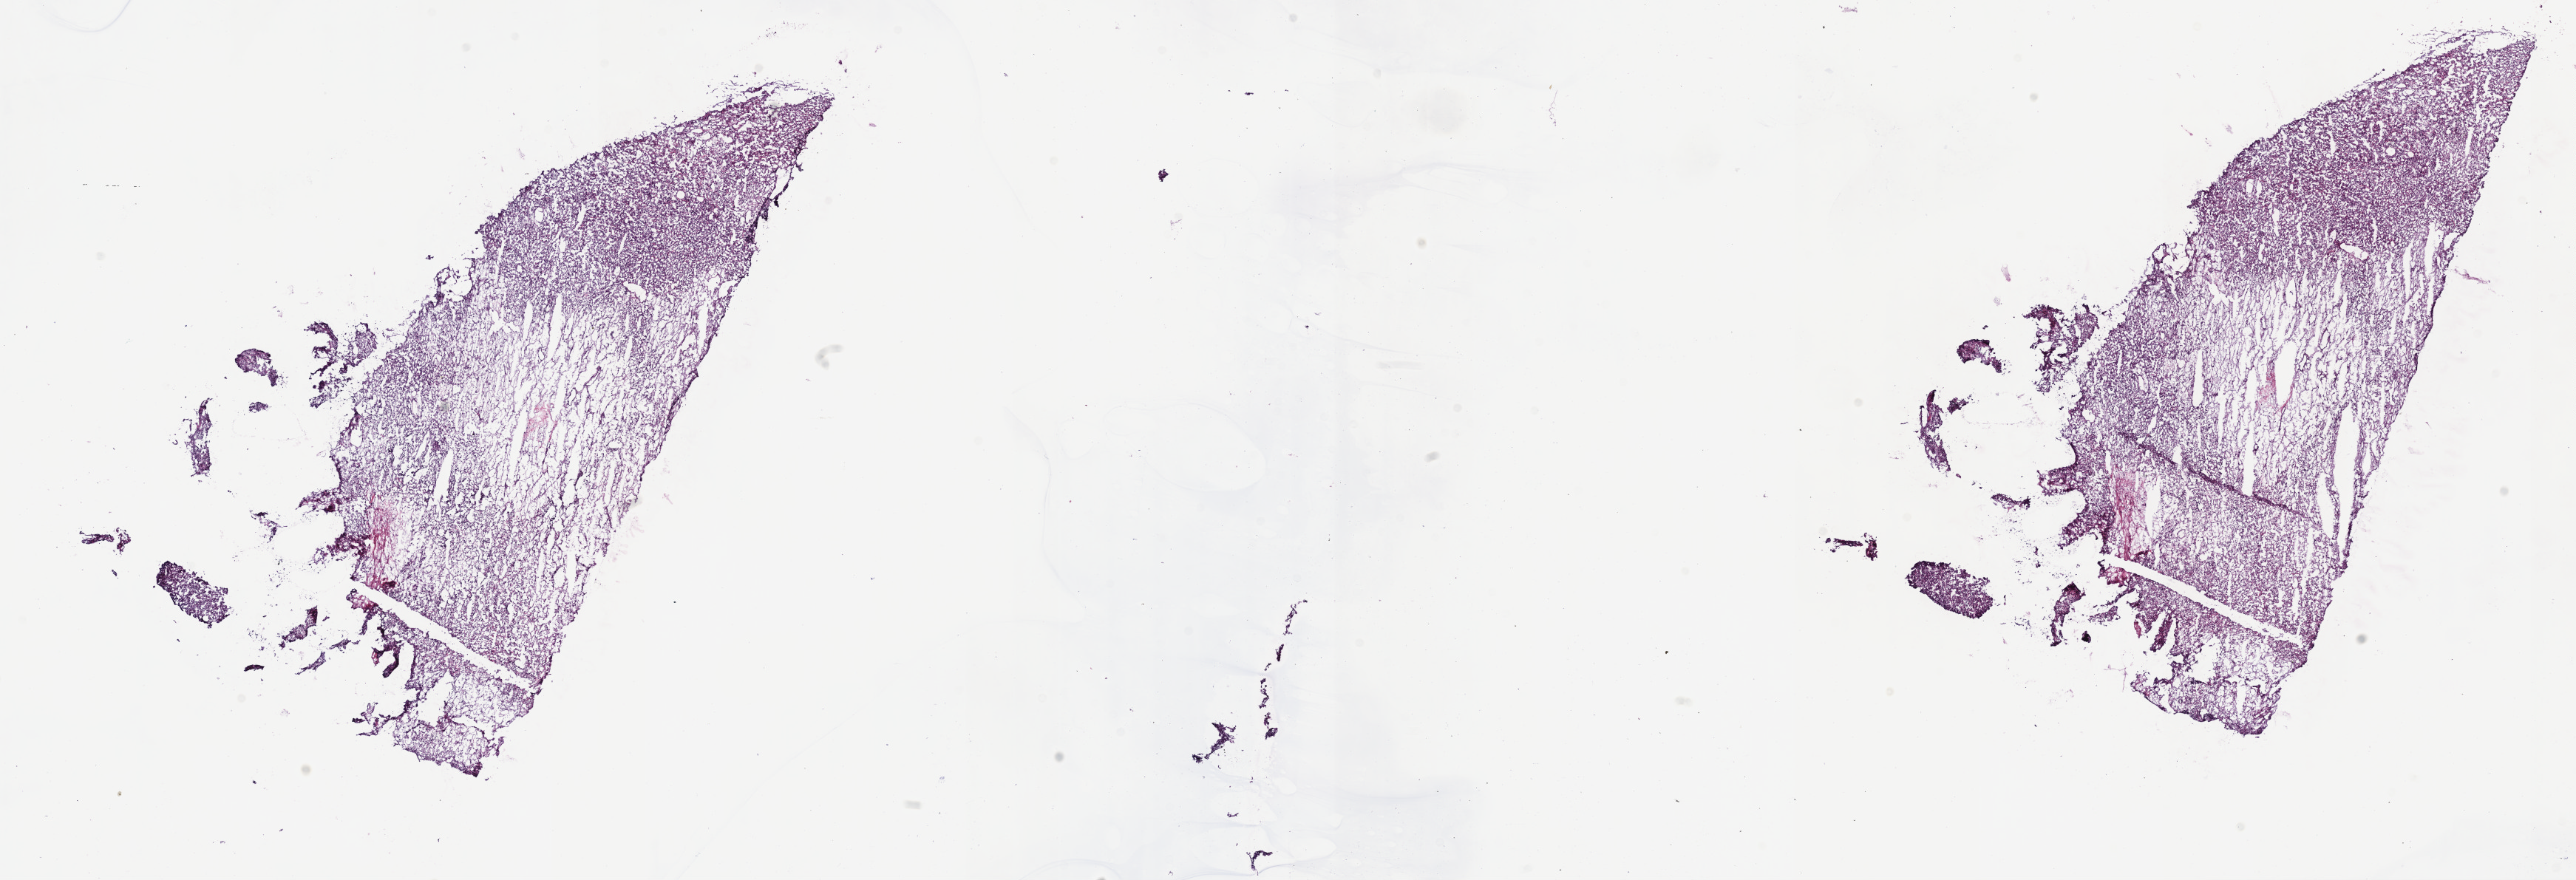
Digitized Hematoxylin and eosin (H&E) stained tissue section (whole slide) — a low-resolution overview of the entire scanned area, about 28.2 x 9.6 mm, frozen section, primary tumour sample from the kidney. Patient: male, age at initial diagnosis 69 years. Histologic grade: G2 (moderately differentiated). Pathologist review of this section (percent, as recorded): tumour cells 72%, tumour nuclei 92%, normal cells 0%, stromal cells 10%, necrosis 18%. Inflammatory infiltration, as recorded: lymphocyte infiltration 3%, monocyte infiltration 1%, neutrophil infiltration 1%.
Pathologic diagnosis: Clear cell adenocarcinoma, NOS. TNM: T1a N0 M0. AJCC pathologic stage: I (7th edition).